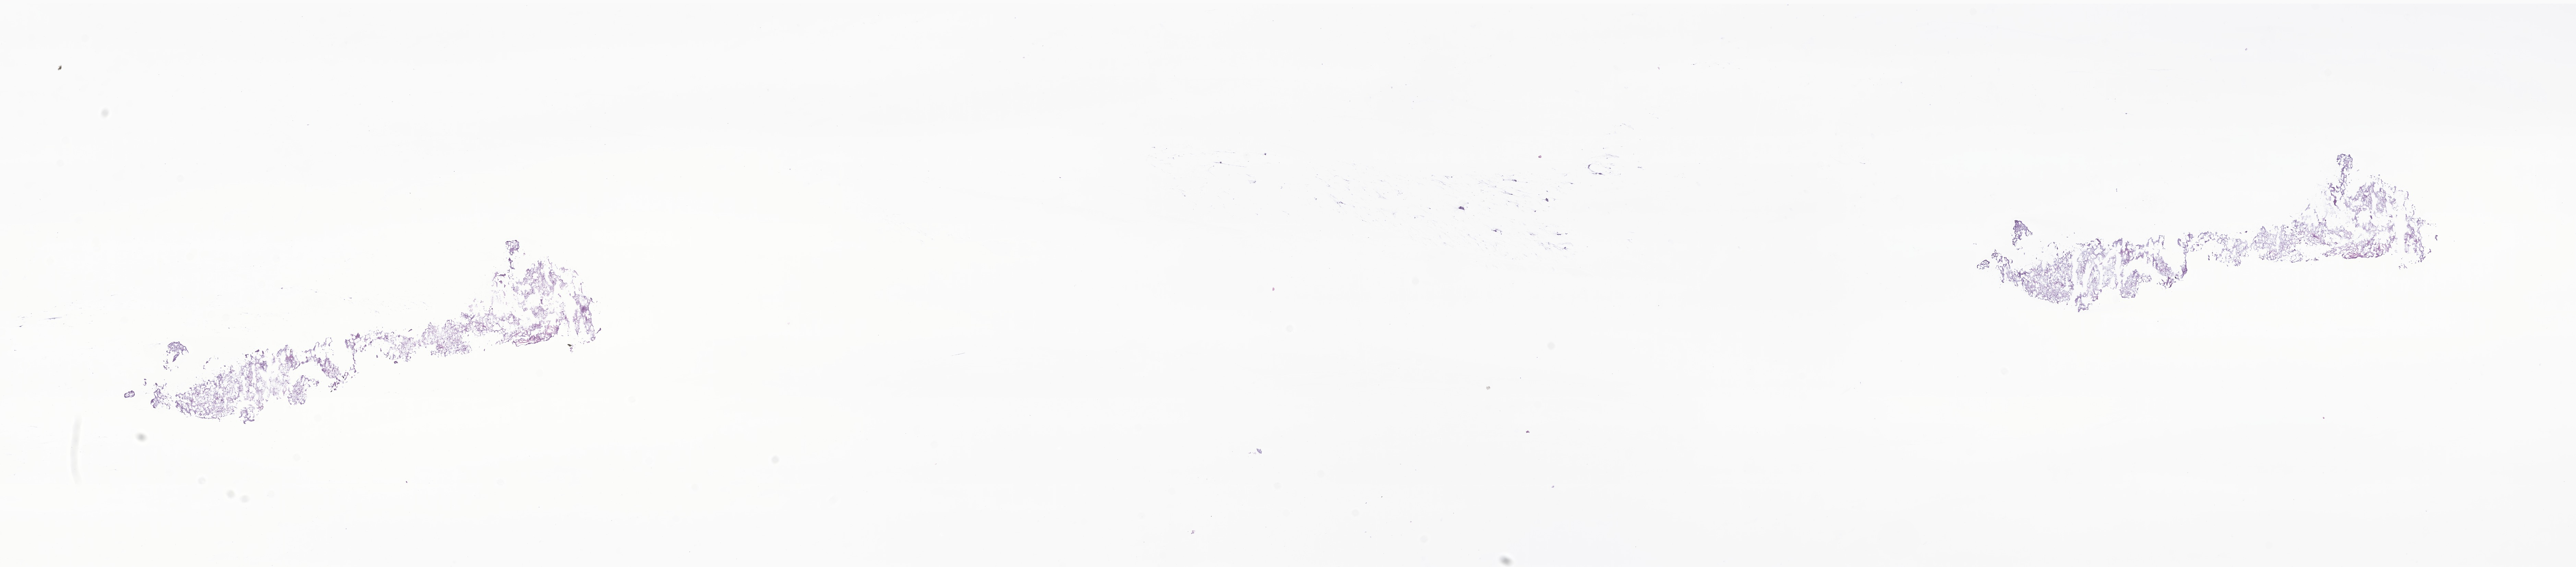
Haematoxylin and eosin whole-slide image of tumor tissue from the cerebellum, a low-resolution overview of the entire scanned area, about 31.7 x 7.0 mm, frozen section. Patient female; age 621 days.
* diagnosis (ICD-O-3 morphology term): Pilocytic astrocytoma